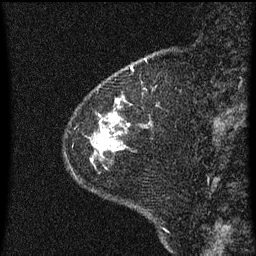
Breast MRI (dynamic contrast-enhanced), one sagittal slice; position 12 of 60 along the scan axis; dynamic contrast-enhanced series, image 2 of 3 at this slice position (ordered by acquisition); 1.5 T; TE 4.2 ms, TR 8 ms; 2 mm slice thickness; 256 × 256 image matrix. Female patient, age 60 years.
Structures marked on this image (semi-automatic segmentation, software-assisted and operator-edited):
- analysis volume of interest (the breast-tissue region the enhancement analysis was run in; not a lesion): bounding box [x1, y1, x2, y2] px = [92, 90, 132, 167]
- tumour enhancement mask (voxels above the 70 % enhancement threshold inside the analysis volume of interest): [92, 100, 119, 161]